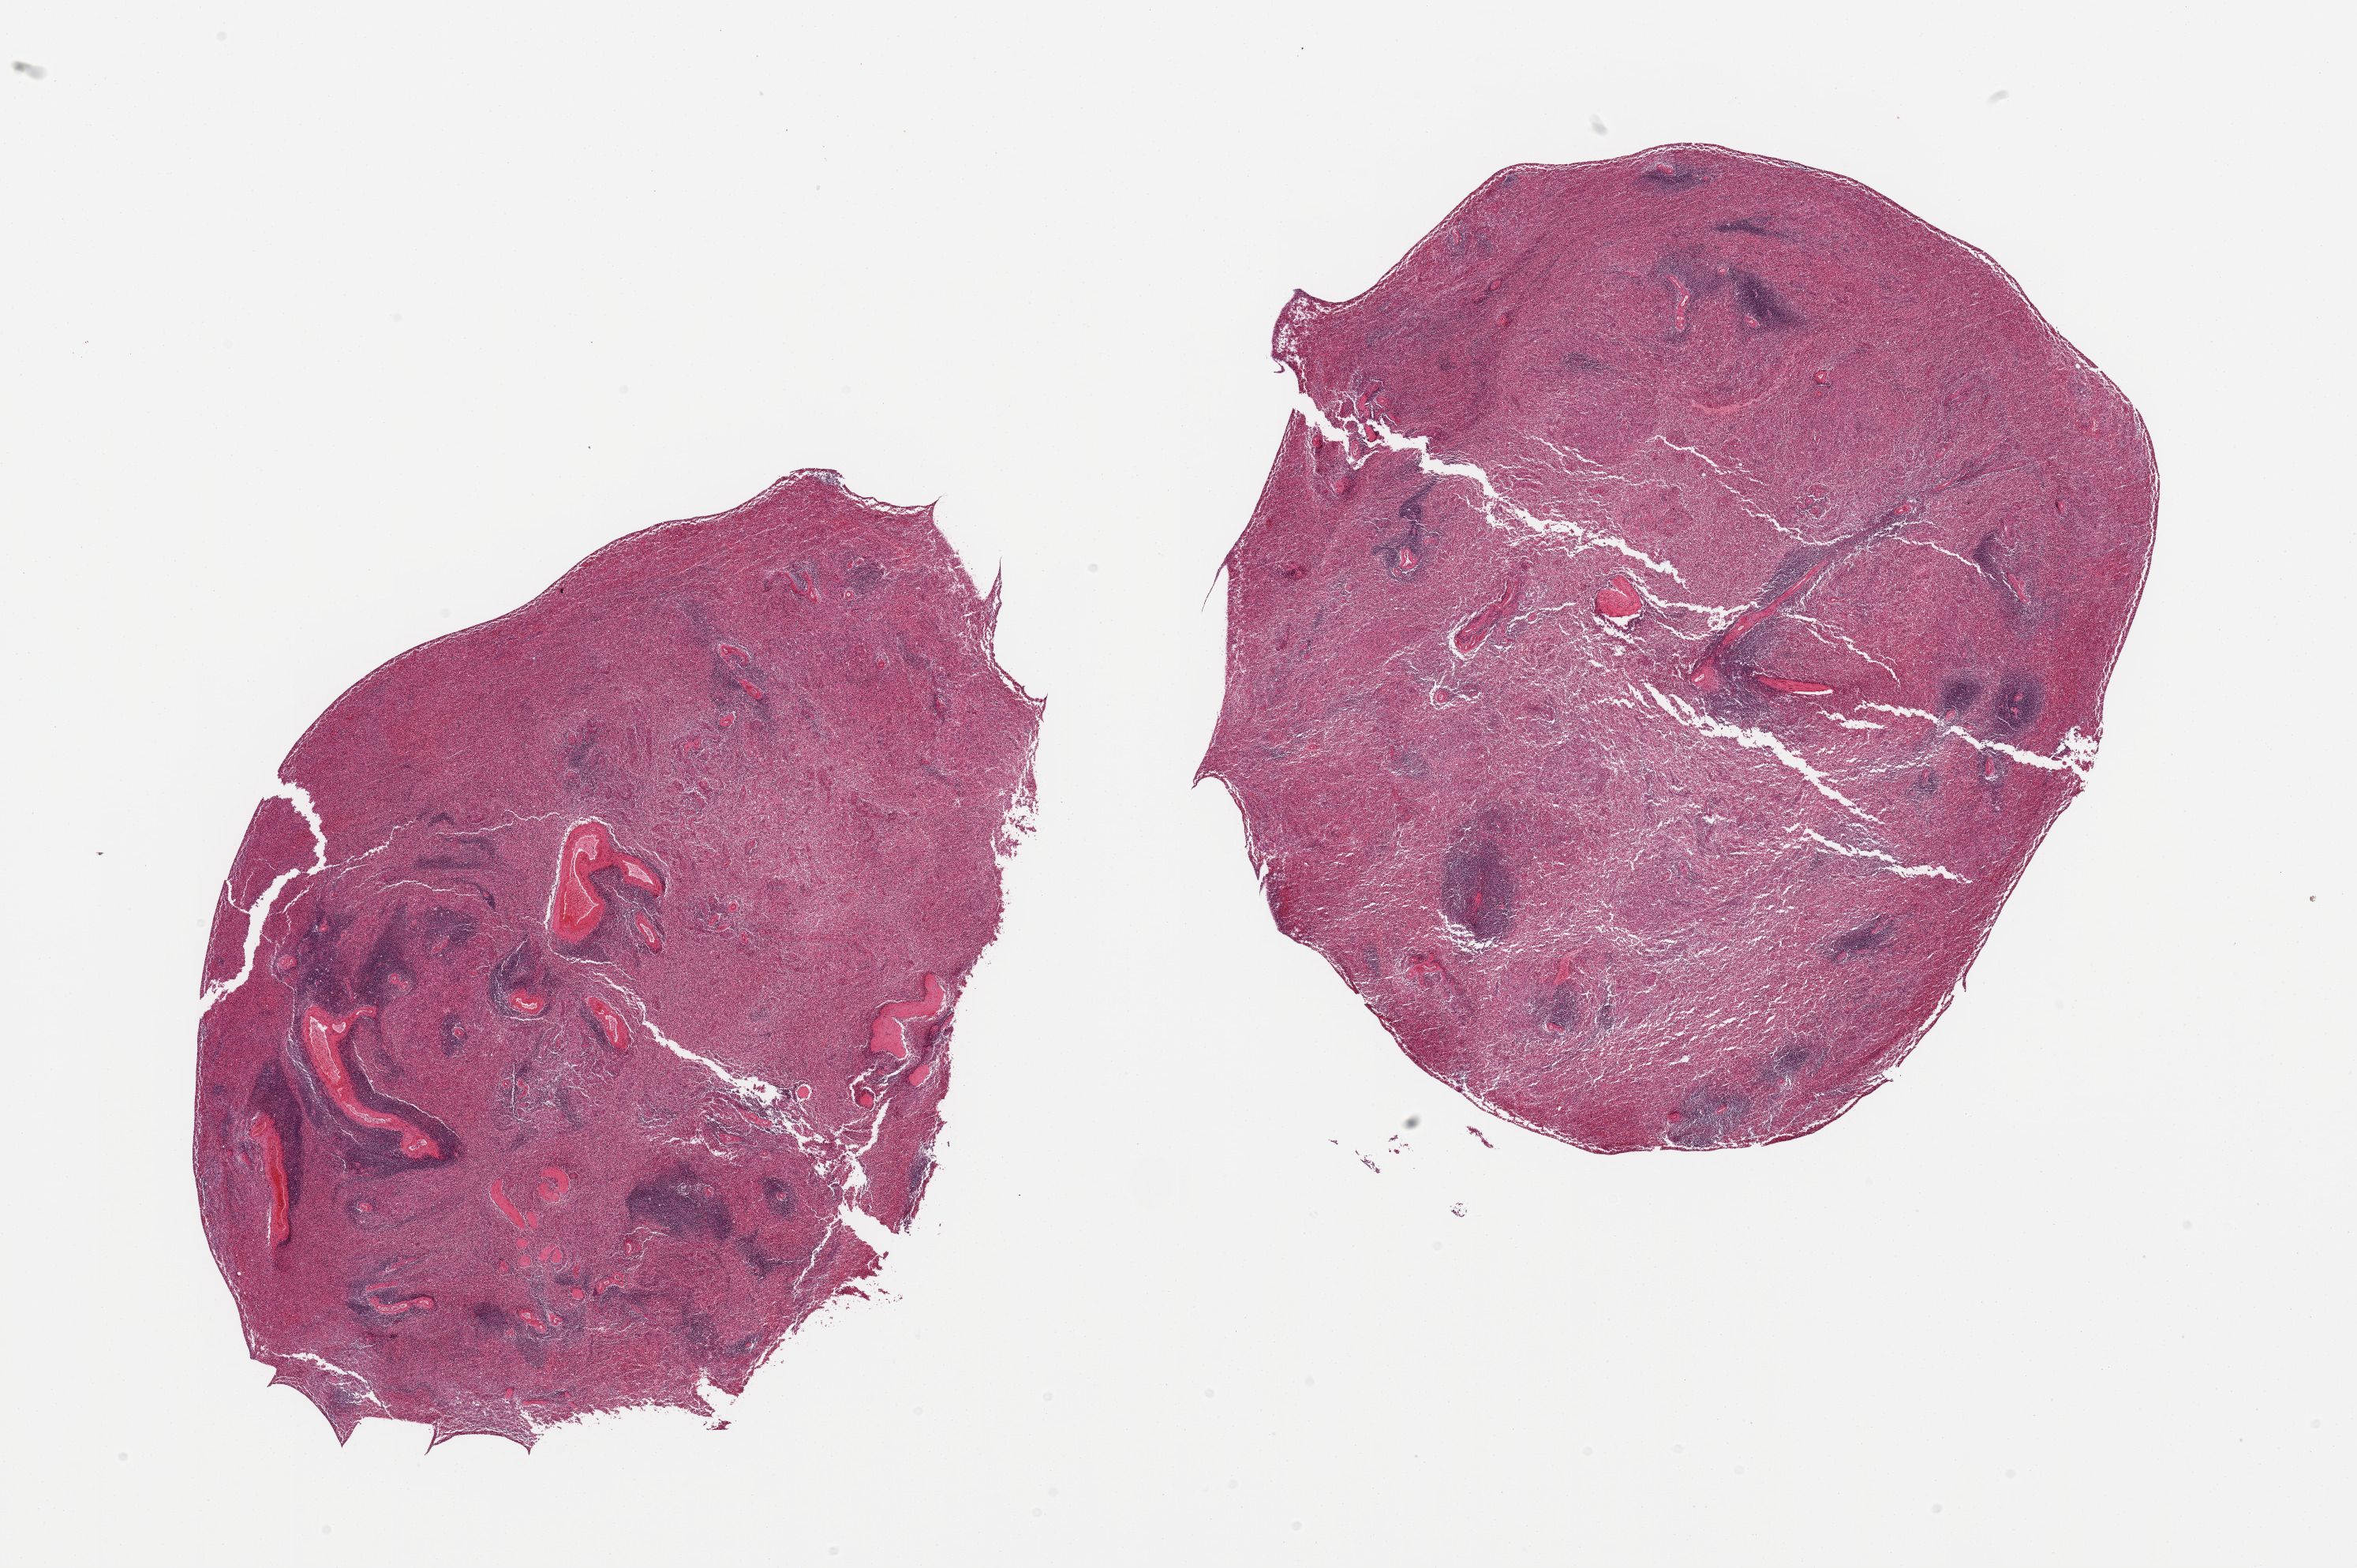
Haematoxylin and eosin whole-slide image — whole scanned area (about 23.6 x 15.7 mm, acquisition: 20x scan) shown as a low-resolution overview. PAXgene-fixed paraffin-embedded (PFPE) section. Sampled site (target tissue): spleen. Tissue donor sample. Donor sex: male.
Reviewer comment on this tissue sample: 2 pieces, no abnormalities.